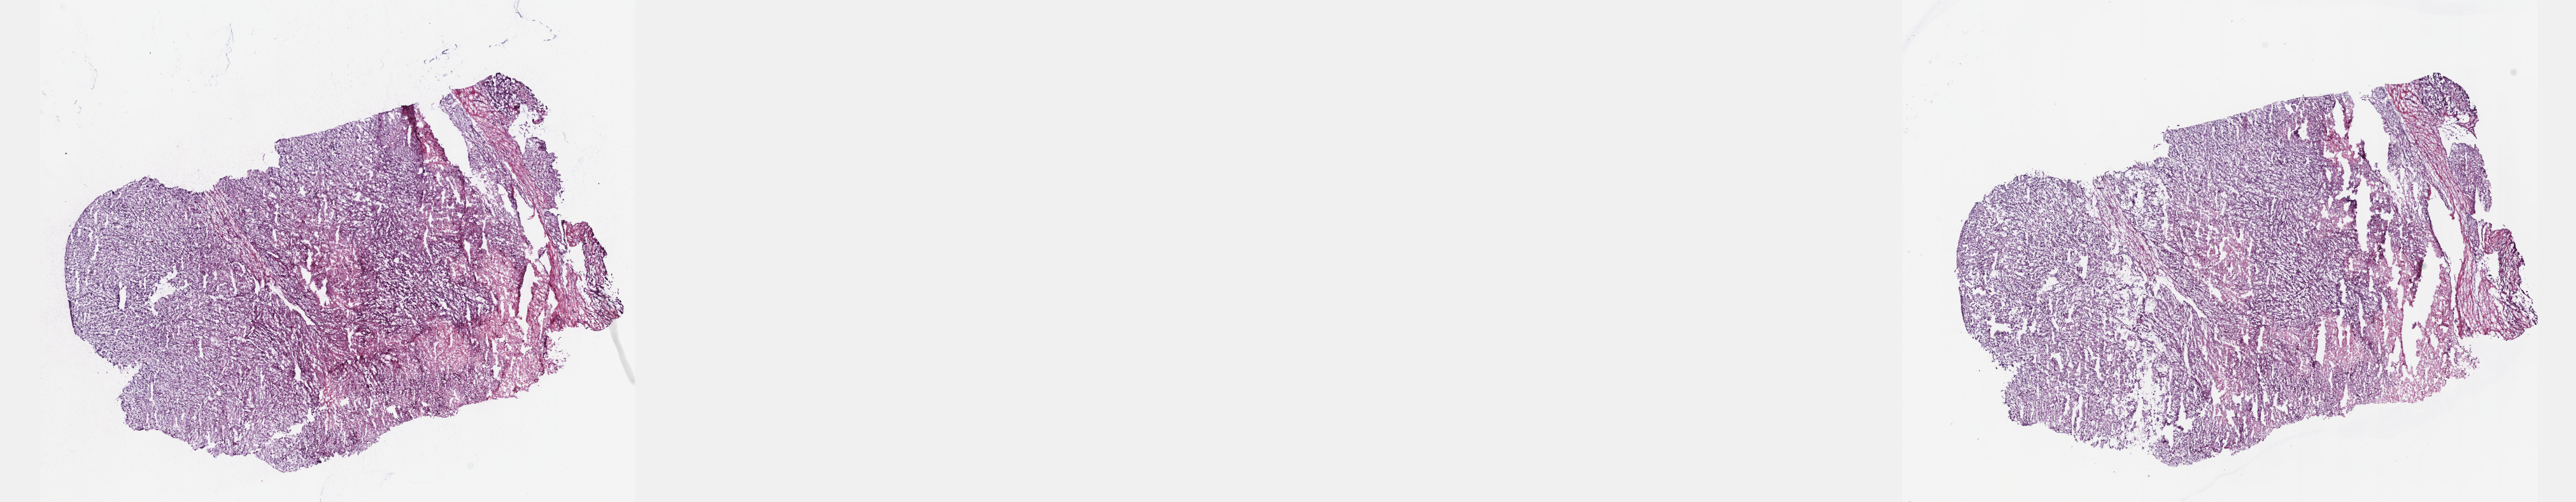
Digitized Hematoxylin and eosin (H&E) stained tissue section (whole slide), shown as a low-resolution overview of the whole scanned area (about 32.7 x 6.4 mm, slide scanned at 40x). Frozen section. Primary tumour sample from the liver. Female patient; age at initial diagnosis 49 years. Histologic grade: G3 (poorly differentiated). Composition of this section per pathologist review: tumour cells 75%, tumour nuclei 75%, normal cells 0%, stromal cells 15%, necrosis 10%. Inflammatory infiltration, as recorded: lymphocyte infiltration 3%, monocyte infiltration 1%, neutrophil infiltration 2%.
* TNM: T3 N0 M0
* AJCC pathologic stage: IIIB (7th edition)
* diagnosis: Hepatocellular carcinoma, clear cell type